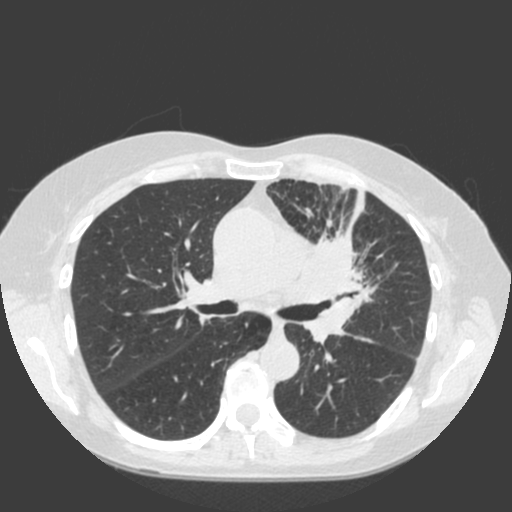
Low-dose screening chest CT, one axial slice. 120 kVp. Lung window (W 1500 / L -600 HU). 2 mm slice thickness. 512 × 512 image matrix.
Structures marked on this image (manually delineated by an expert):
- lesion 1 (tumor, hilum of left lung): box from (x=294, y=231) to (x=377, y=346) px